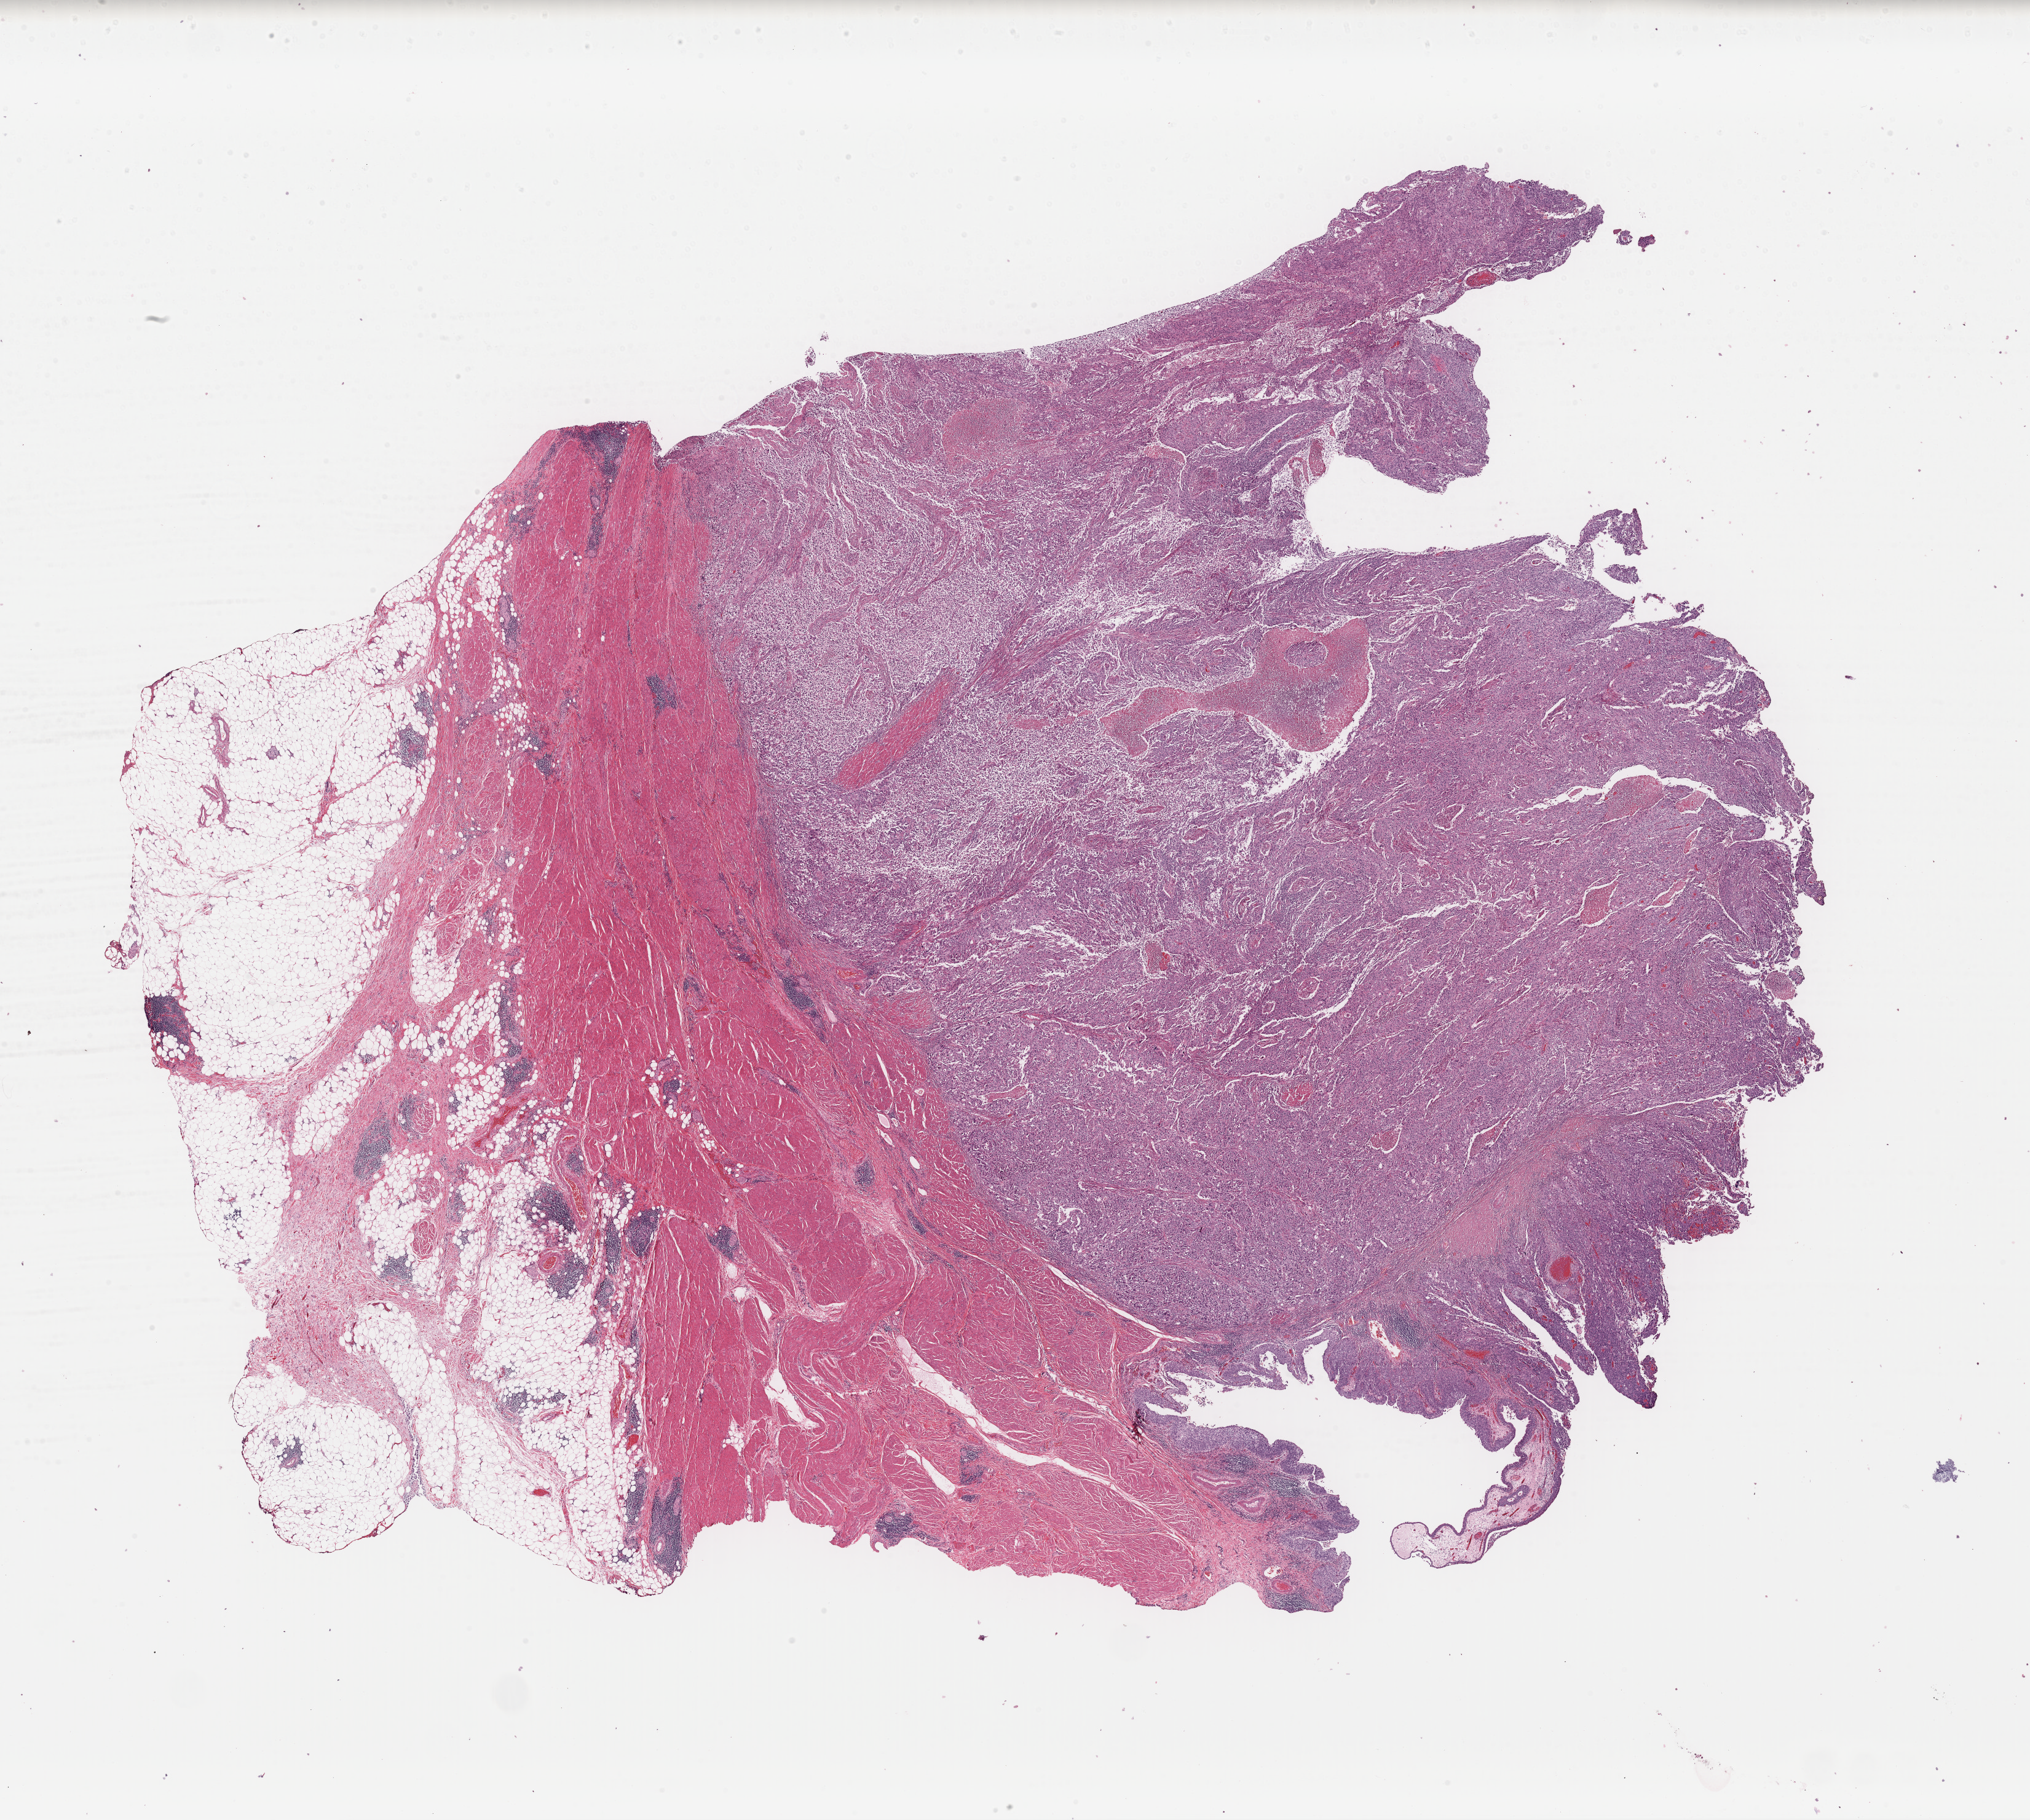
Hematoxylin and eosin (H&E) stained whole-slide image — shown as a low-resolution overview of the whole scanned area (about 26.1 x 23.4 mm). FFPE section. Sample: primary tumour, bladder. Male patient; age at initial diagnosis 72 years. Histologic grade: high grade.
Histologic diagnosis: Transitional cell carcinoma (trigone of bladder). Lymph nodes positive (case pathology): 0 of 11 examined. AJCC pathologic stage: III (6th edition).